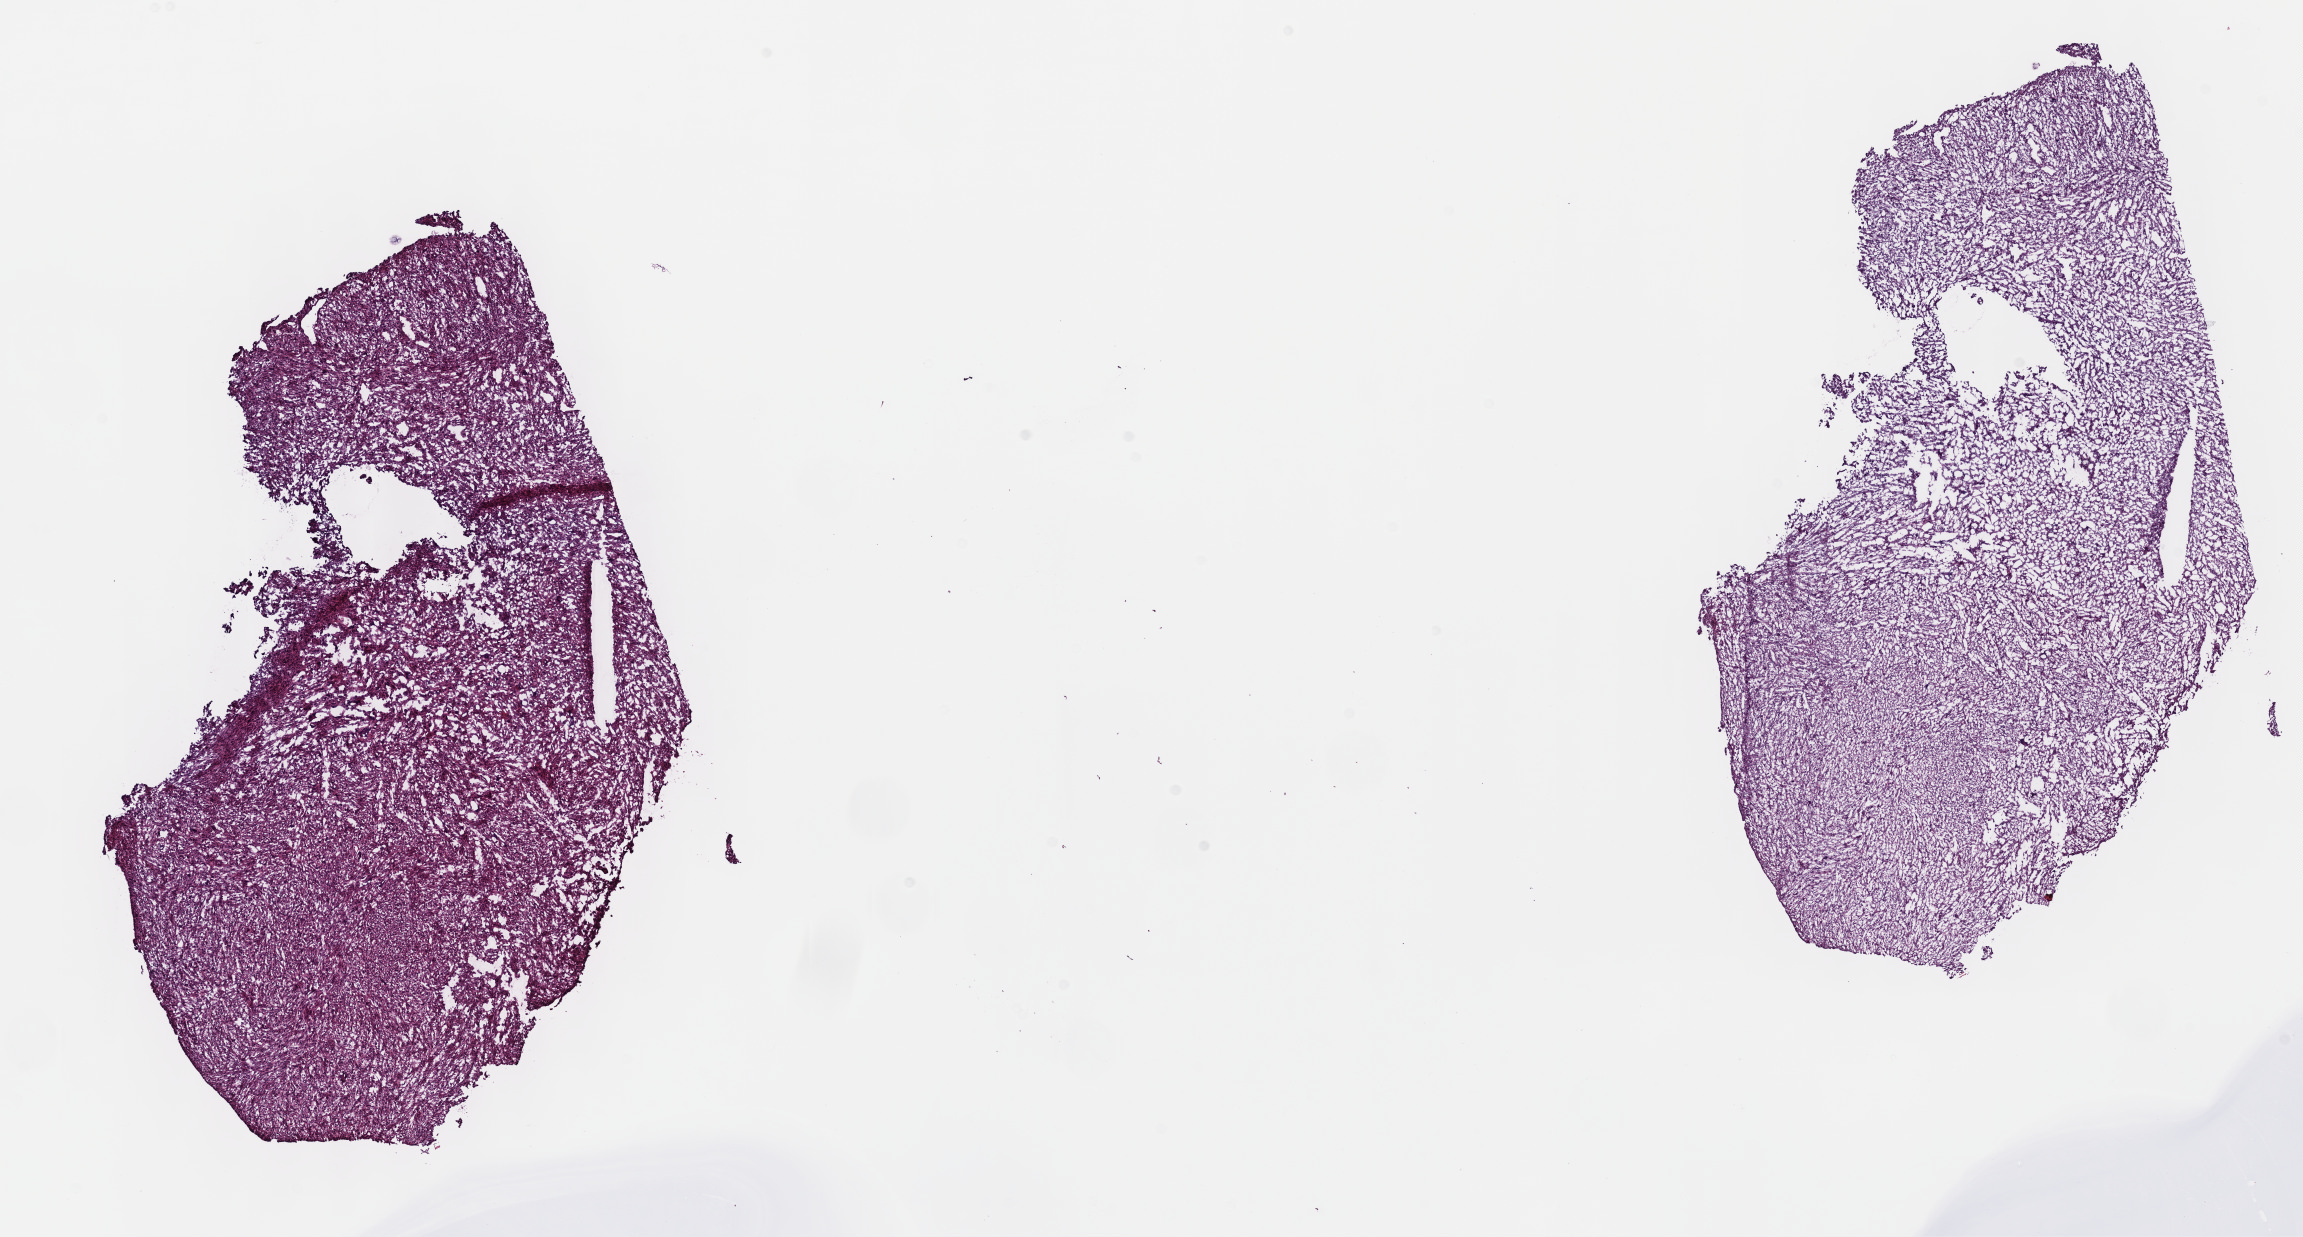
Whole-slide histology image, Hematoxylin and eosin (H&E) stained — shown as a low-resolution overview of the whole scanned area (about 18.6 x 10.0 mm, from a 40x scan); frozen section from the top of the tissue portion; sample: primary tumour, retroperitoneum and peritoneum. Female, age 64 years at initial diagnosis. Pathologist review of this section (percent, as recorded): tumour cells 80%, tumour nuclei 100%, normal cells 0%, stromal cells 20%, necrosis 0%. Inflammatory infiltration, as recorded: lymphocyte infiltration 0%, monocyte infiltration 0%, neutrophil infiltration 0%.
Histologic diagnosis: Undifferentiated sarcoma (retroperitoneum).